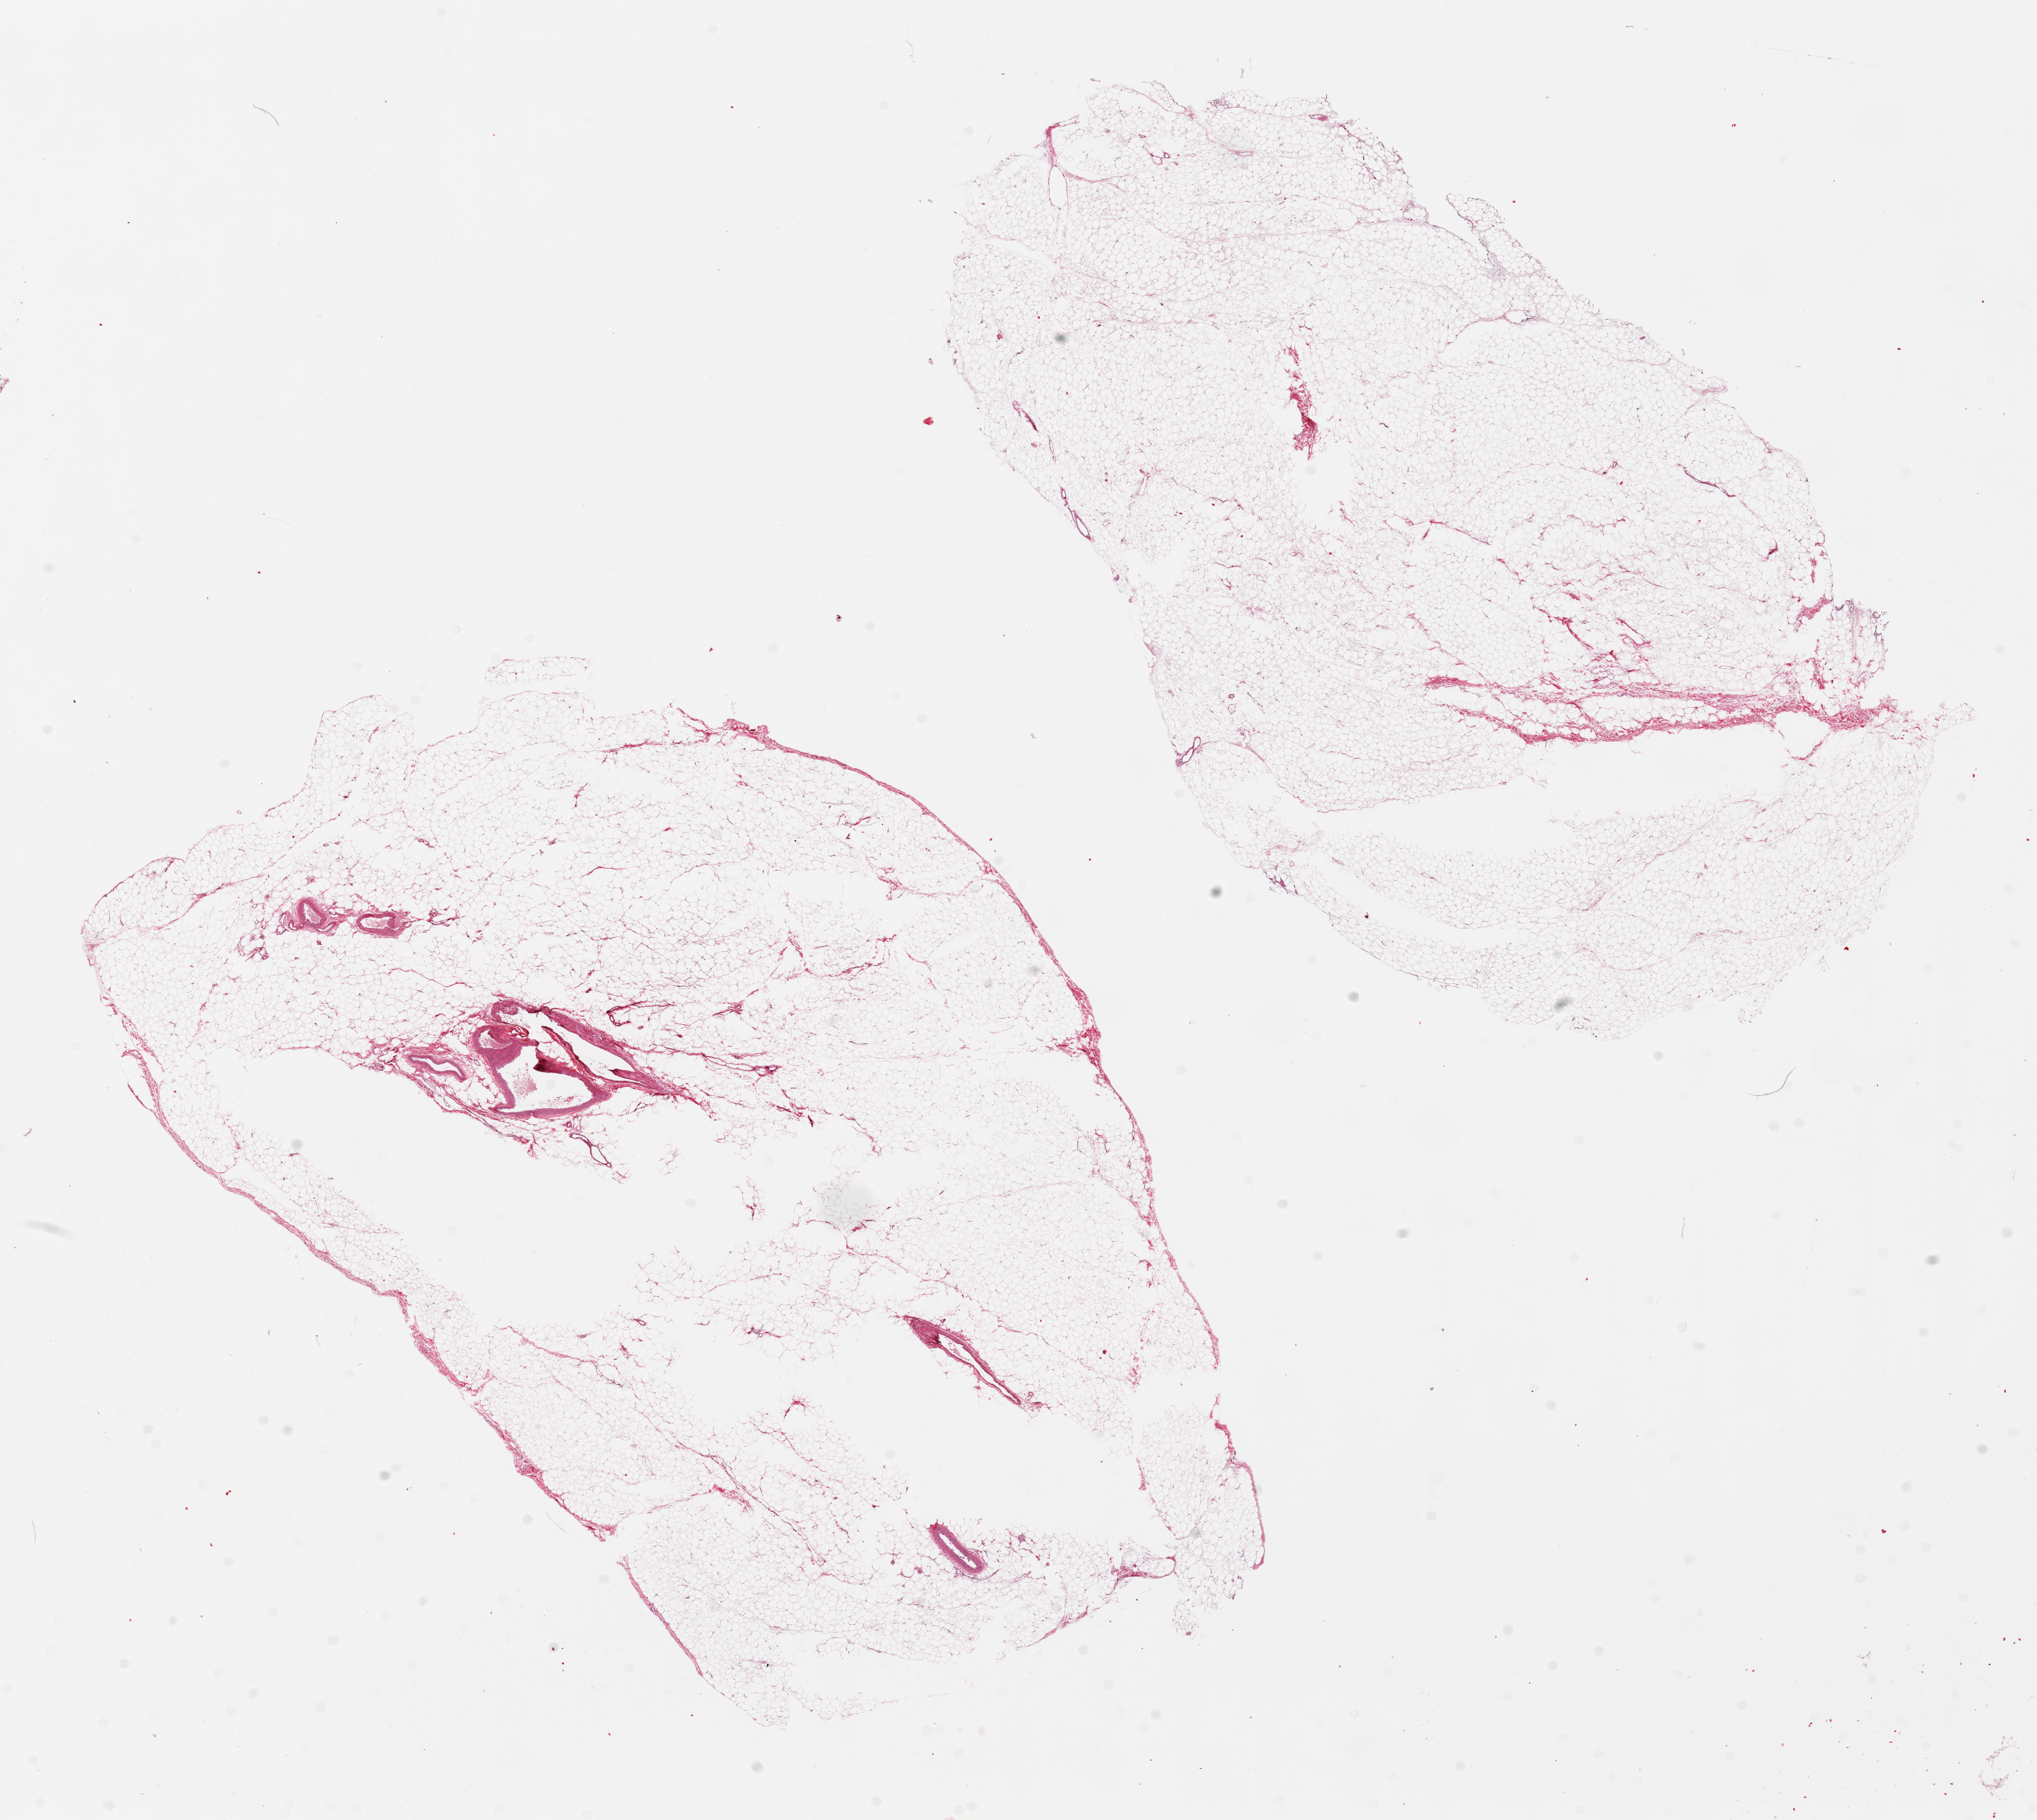
Whole-slide image, haematoxylin and eosin stain, brightfield, shown as a low-resolution overview of the whole scanned area (about 23.6 x 21.1 mm, acquisition: 20x scan); PAXgene-fixed paraffin-embedded (PFPE) section; section of omentum (target tissue); tissue donor sample. Donor sex: male.
Review note (as recorded): 2 pieces, not atrial appendage as originally labeled; adipose tissue,with central defects (? incomplete fixation), tissue exceeds recommended size.